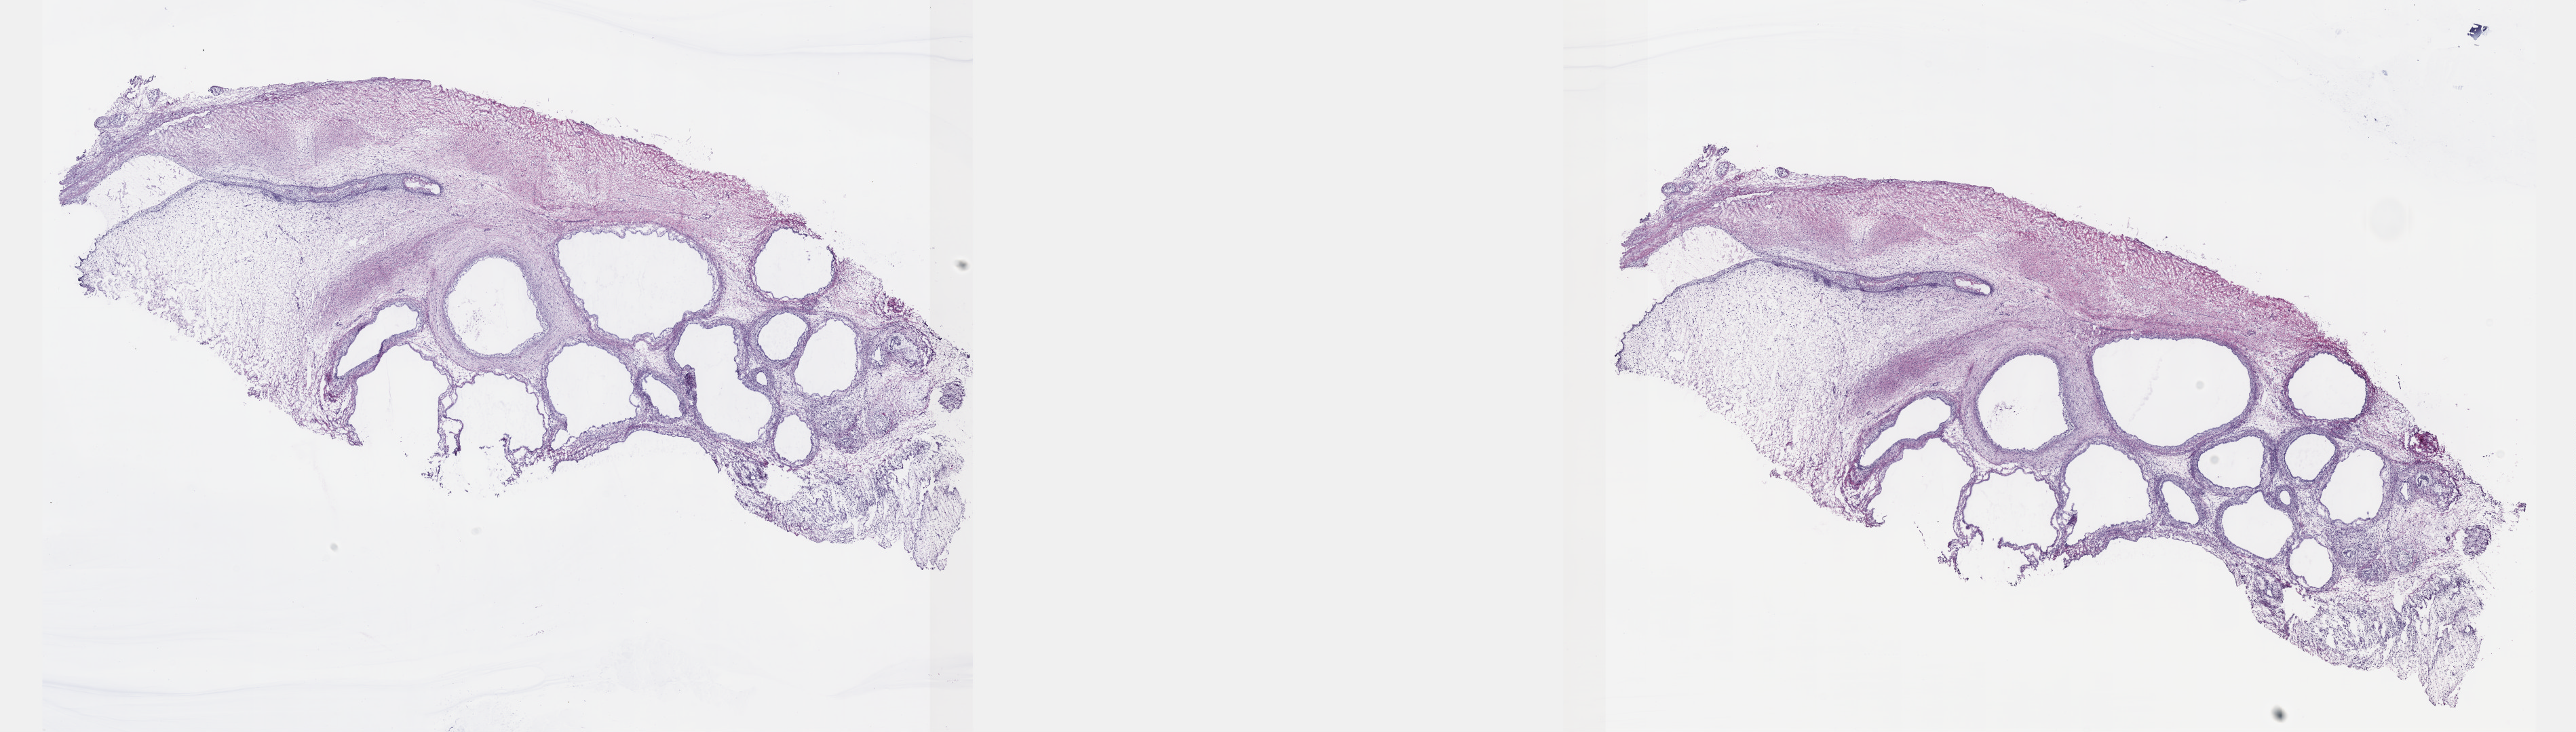
Digitized Hematoxylin and eosin (H&E) stained tissue section (whole slide) — whole scanned area (about 30.7 x 8.7 mm, acquisition: 40x scan) shown as a low-resolution overview. Frozen section from the top of the tissue portion. Testis, primary tumour sample. Patient: male, age at initial diagnosis 22 years. Slide review estimates, as recorded: tumour cells 100%, tumour nuclei 80%, normal cells 0%, stromal cells 0%, necrosis 0%. Inflammatory infiltration, as recorded: lymphocyte infiltration 1%, monocyte infiltration 0%, neutrophil infiltration 0%.
AJCC pathologic stage: IA (5th edition). Histologic diagnosis: Teratoma, benign.